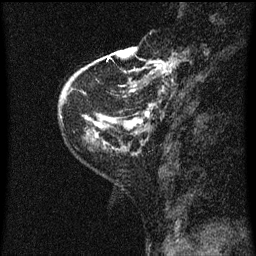
Breast MRI (dynamic contrast-enhanced), one sagittal slice. Position 14 of 60 along the scan axis. Dynamic contrast-enhanced series, image 2 of 3 at this slice position (ordered by acquisition). 1.5 T. TE 4.2 ms, TR 8 ms. 2 mm slice thickness. 256 × 256 image matrix. Patient: female, 48 years.
Annotated regions visible in this slice (semi-automatically segmented with operator editing):
- analysis volume of interest (the breast-tissue region the enhancement analysis was run in; not a lesion): bounding box [x1, y1, x2, y2] px = [128, 54, 174, 125]
- tumour enhancement mask (voxels above the 70 % enhancement threshold inside the analysis volume of interest): [128, 58, 174, 121]